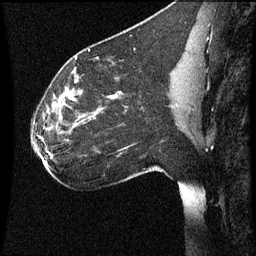
Breast MRI (dynamic contrast-enhanced), one sagittal slice. Dynamic contrast-enhanced series, image 2 of 3 at this slice position (ordered by acquisition). 1.5 T. TE 4.2 ms, TR 8.9 ms. 2 mm slice thickness. 256 × 256 image matrix. Patient: female, 35 years. From the clinical record (not read from this slice): setting: breast cancer imaged before/during neoadjuvant chemotherapy; receptor status: HER2-positive.
Outlined on this slice (semi-automatic segmentation, software-assisted and operator-edited):
- analysis volume of interest (the breast-tissue region the enhancement analysis was run in; not a lesion): box from (x=29, y=66) to (x=177, y=177) px
- tumour enhancement mask (voxels above the 70 % enhancement threshold inside the analysis volume of interest): (x=63, y=92)–(x=117, y=107)